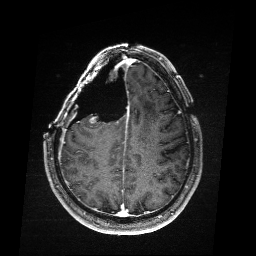
Brain MRI from a brain-tumour surgery series, one axial slice; position 68 of 176 along the scan axis; T1-weighted post-contrast; 256 × 256 image matrix. Case-level facts recorded for this patient, not image findings: histopathology: Astrocytoma; WHO grade: 4; IDH mutation: yes.
Annotated regions visible in this slice (manually delineated by an expert):
- residual tumour: box from (x=106, y=117) to (x=112, y=124) px